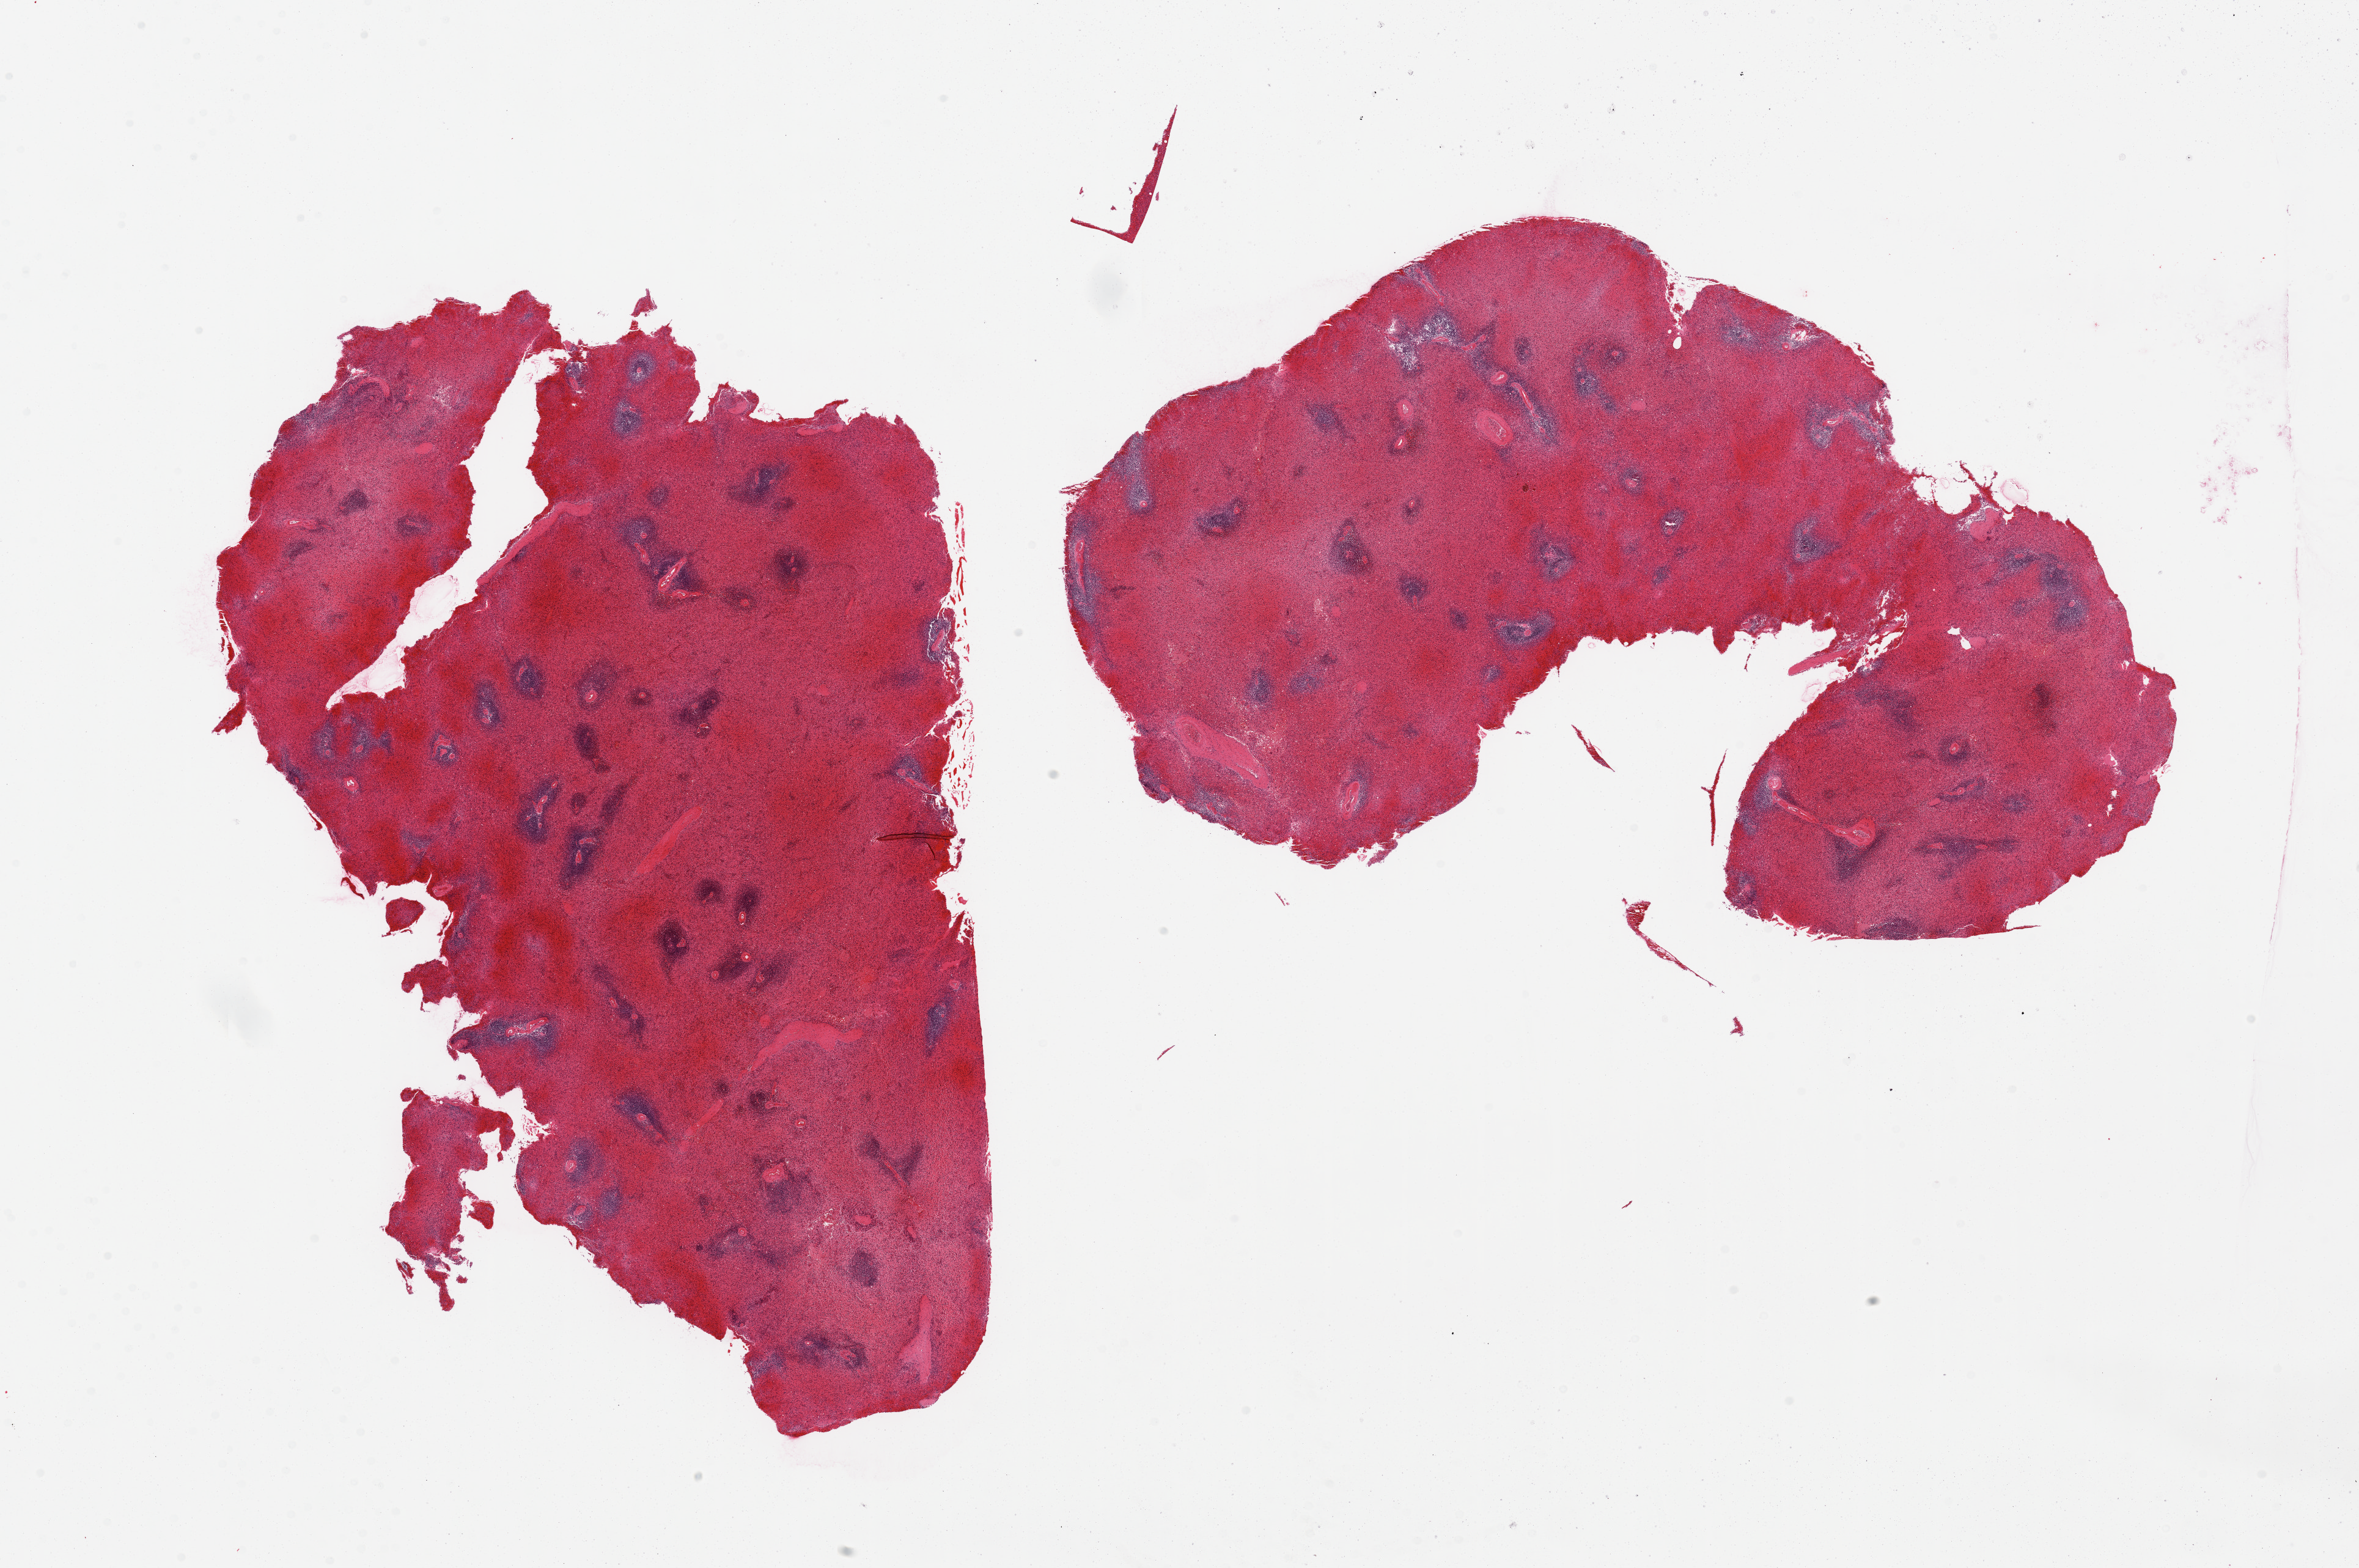
Digitized hematoxylin and eosin (H&E)-stained section — a low-resolution overview of the entire scanned area, about 30.5 x 20.3 mm, PAXgene-fixed paraffin-embedded (PFPE) section, target tissue: spleen, tissue donor sample. Donor sex: male.
Review note (as recorded): 2 pieces, congested.